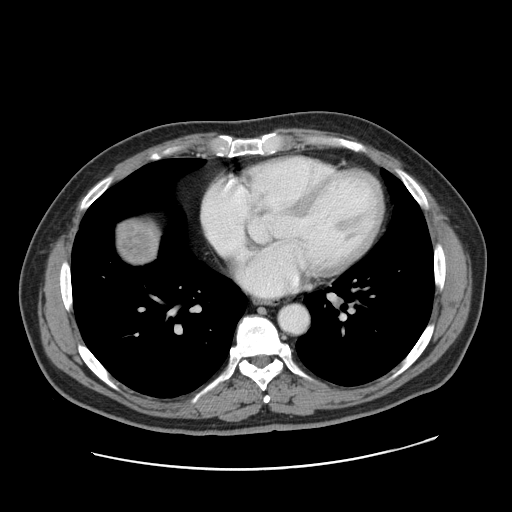
Contrast-enhanced abdominal CT, one axial slice; slice 168 of 178 in the series (ordered by position); intravenous contrast given; soft-tissue window (W 400 / L 40 HU); 2.5 mm slice thickness; 512 × 512 image matrix, field of view 403 × 403 mm. Male patient, age 63 years. Case-level facts recorded for this patient, not image findings: diagnosis: colorectal cancer liver metastases, imaged before liver resection; multiple liver metastases: yes; largest metastasis: 8 cm.
Annotated regions visible in this slice (outlined manually by an expert reader):
- liver: bounding box [x1, y1, x2, y2] px = [117, 219, 158, 263]
- liver metastasis: [121, 222, 159, 262]